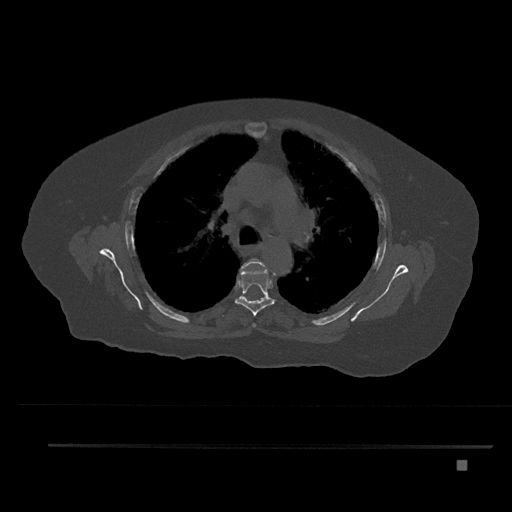
CT including the spine, one axial slice; position 570 of 797 along the scan axis; bone window (W 1800 / L 400 HU); 0.5 mm slice thickness; 512 × 512 image matrix. Patient: female, 76 years. Case-level facts recorded for this patient, not image findings: primary cancer: lung.
Annotated regions visible in this slice (semi-automatic segmentation, software-assisted and operator-edited):
- T4 vertebra: bounding box [x1, y1, x2, y2] px = [240, 258, 266, 328]
- T5 vertebra: [234, 268, 276, 316]